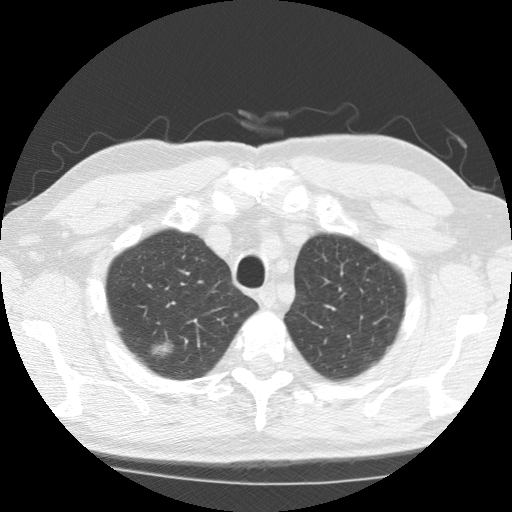
Low-dose screening chest CT, one axial slice; slice 161 of 196 in the series (ordered by position); 120 kVp; lung window (W 1500 / L -600 HU); 2.5 mm slice thickness; 512 × 512 image matrix, field of view 350 × 350 mm.
Structures marked on this image (outlined manually by an expert reader):
- lesion 1 (tumor, upper lobe of right lung): bounding box [x1, y1, x2, y2] px = [154, 345, 169, 354]